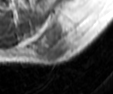
MRI of an extremity soft-tissue mass, one axial slice; position 31 of 42 along the scan axis; MR volume resampled by the dataset authors to the PET/CT grid (not the native acquisition matrix); 3.27 mm slice thickness; 113 × 94 image matrix, field of view 110 × 92 mm. Male patient. Case-level facts recorded for this patient, not image findings: histological type: leiomyosarcoma; grade: intermediate; site of the primary tumour: left pelvis.
Structures marked on this image (expert contour drawn on MRI and transferred to this co-registered scan by the dataset authors):
- gross tumour volume (mass): box from (x=31, y=18) to (x=84, y=65) px